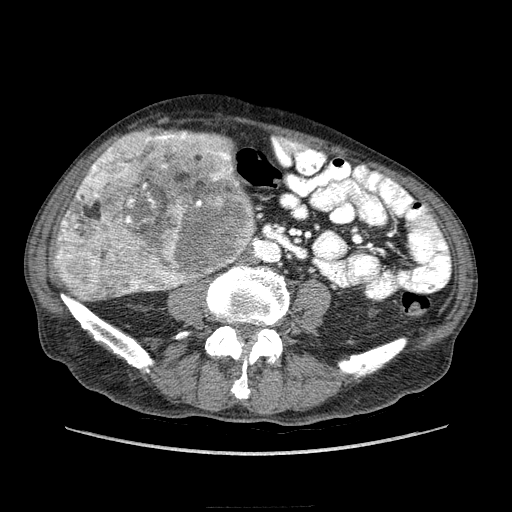
Contrast-enhanced abdominal CT (liver protocol), one axial slice; slice 49 of 218 in the series (ordered by position); reconstruction kernel STANDARD; 100 kVp; soft-tissue window (W 400 / L 40 HU); 2.5 mm slice thickness; 512 × 512 image matrix, field of view 380 × 380 mm. From the clinical record (not read from this slice): diagnosis: hepatocellular carcinoma (patient treated with transarterial chemoembolisation; whether this scan precedes or follows treatment is not stated here); TNM stage (as recorded): Stage-IIIA; Child-Pugh class: A; tumour differentiation: well differentiated; tumour nodularity: multinodular.
Outlined on this slice (semi-automatic segmentation, software-assisted and operator-edited):
- liver parenchyma outside the tumour (the mass and vessels are separate outlines, so this box may not span the whole liver): bounding box <54,130,254,294> (left, top, right, bottom; pixels)
- mass: <54,129,255,301>